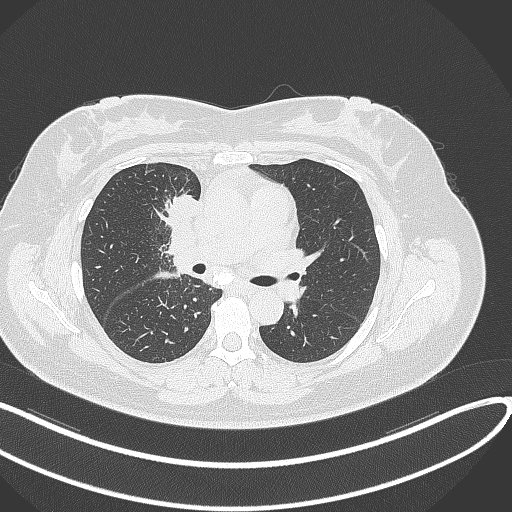
Chest CT, one axial slice. Lung window (W 1500 / L -600 HU). 1 mm slice thickness. 512 × 512 image matrix. Patient: female, 46 years. From the clinical record (not read from this slice): clinical TNM (as recorded): T2a N1 M0.
Outlined on this slice (rectangle marked by the reading radiologist):
- lung tumour (recorded histology: adenocarcinoma): bounding box (x1, y1, x2, y2) in pixels: (169, 189, 198, 221)